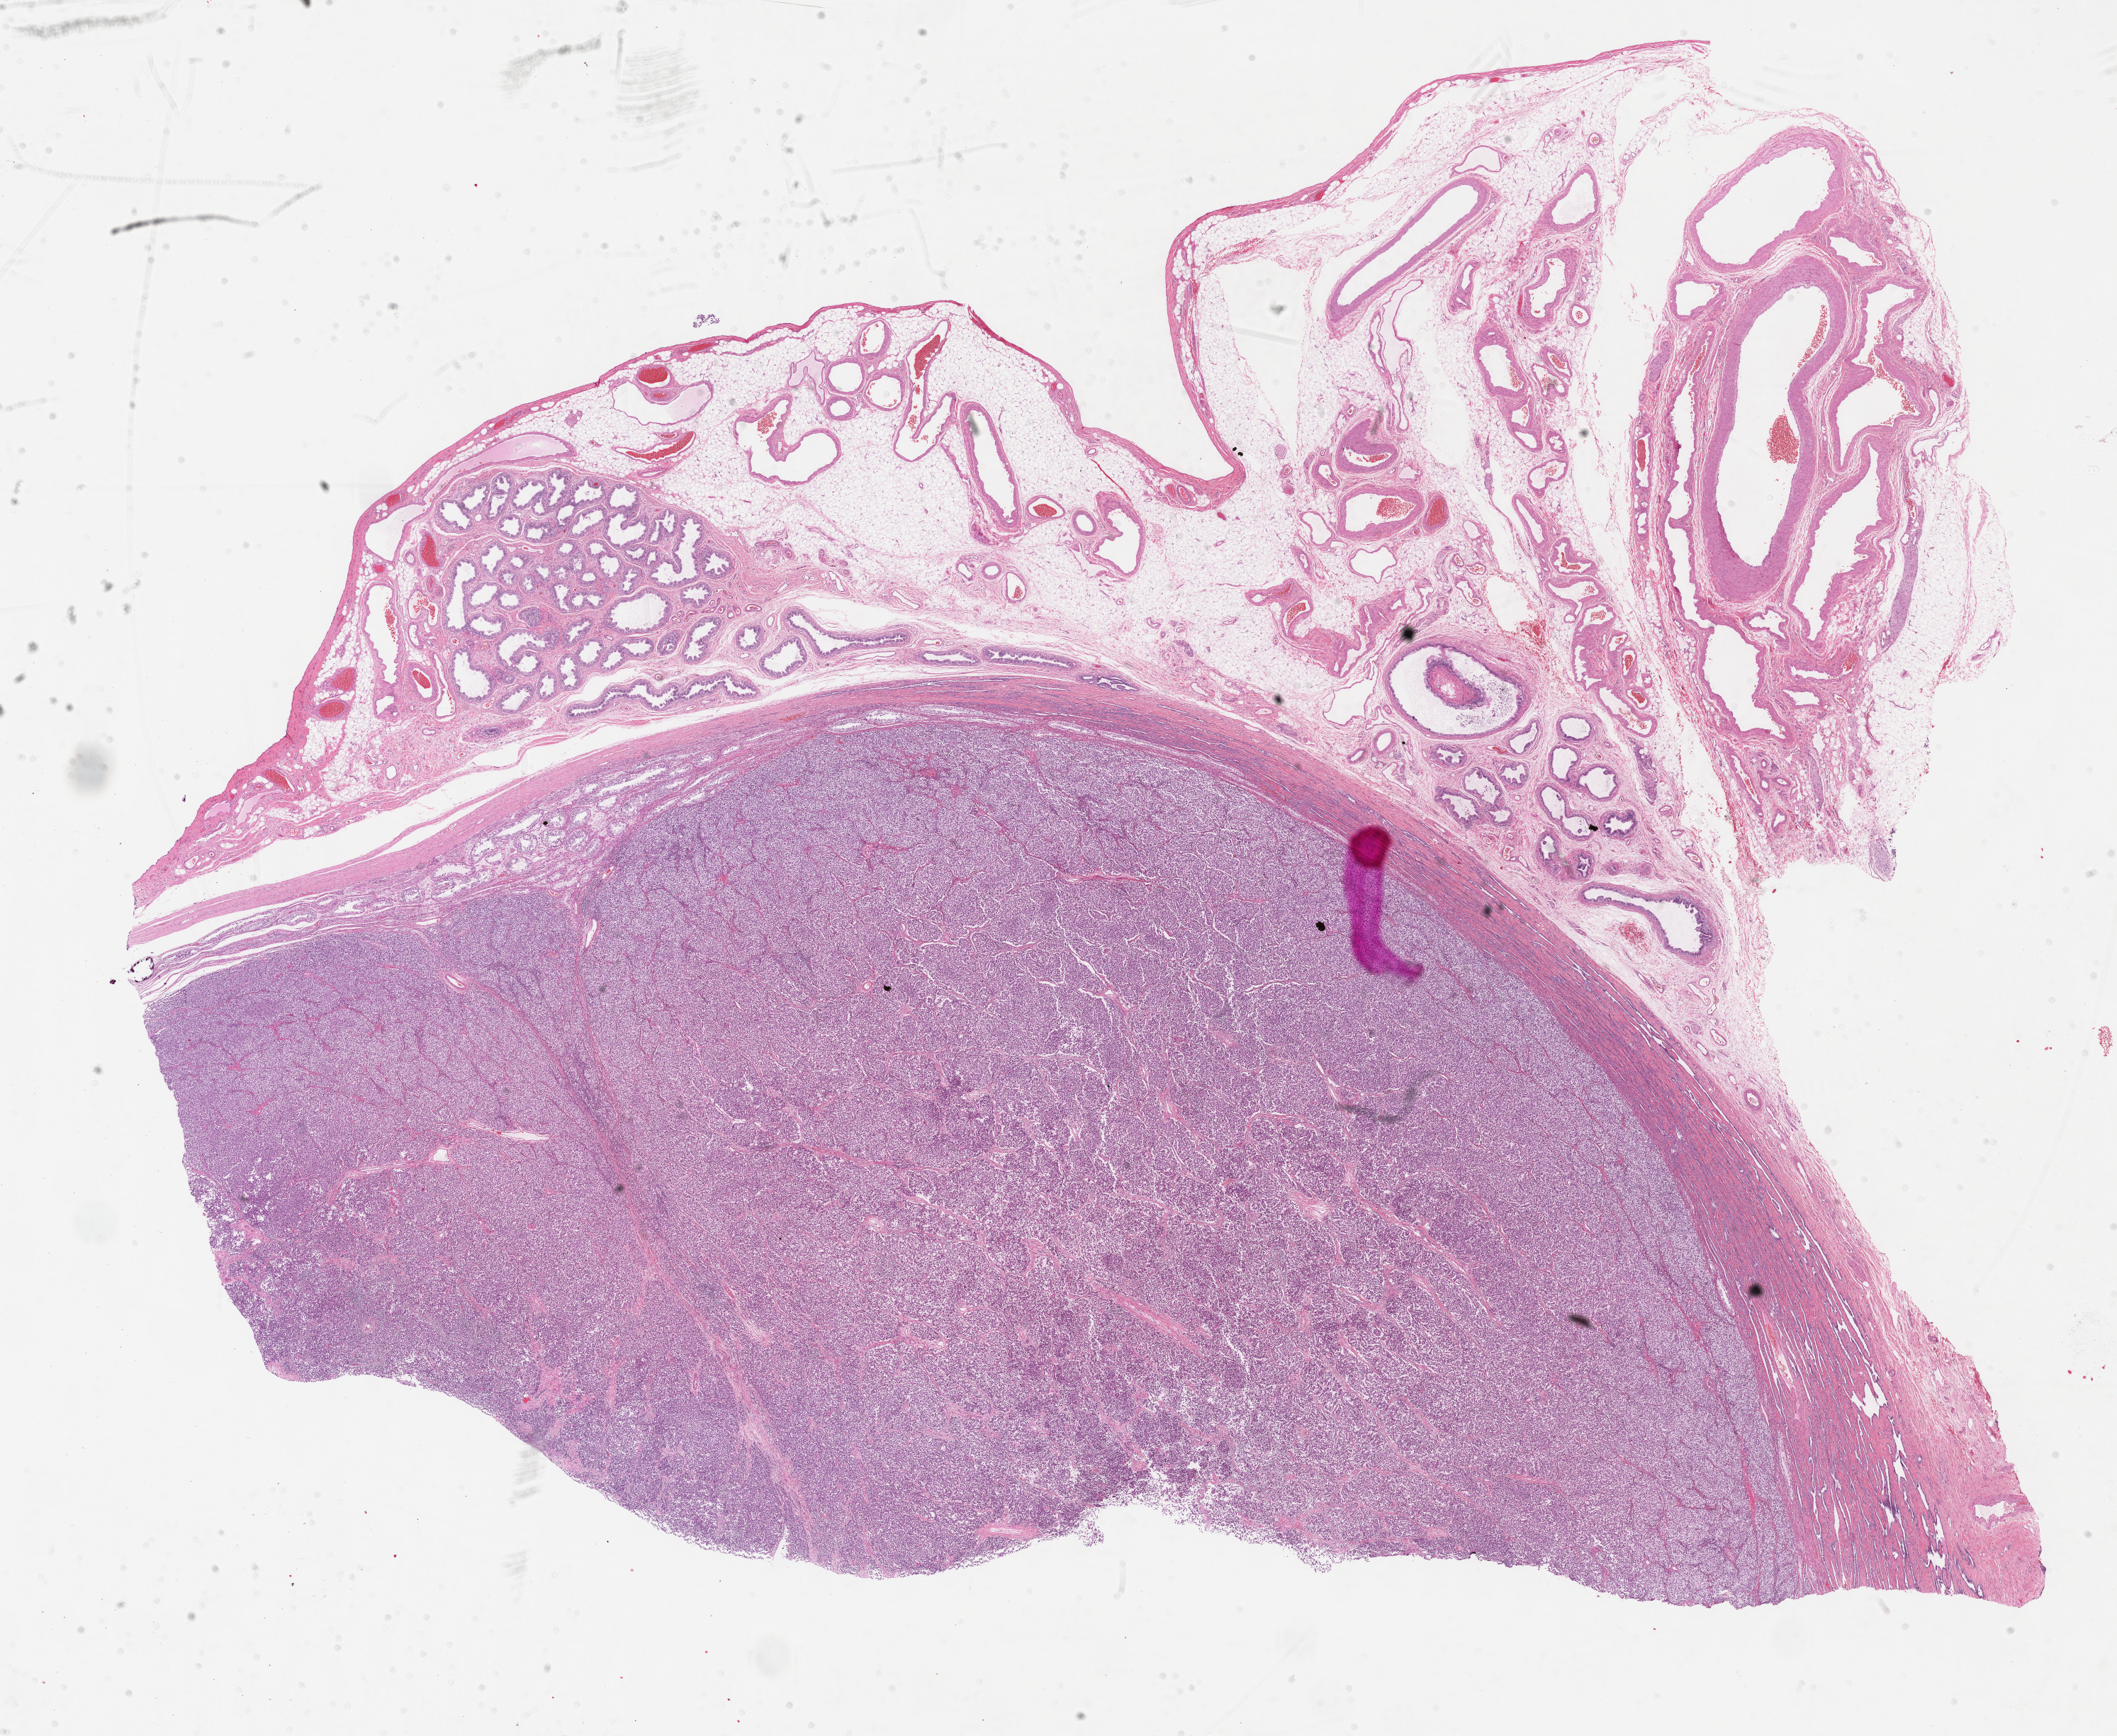
Whole-slide histology image, H&E-stained, whole scanned area (about 24.2 x 19.8 mm, acquisition: 40x scan) shown as a low-resolution overview; formalin-fixed paraffin-embedded (FFPE) diagnostic section; sample: primary tumour, testis. Male, age 38 years at initial diagnosis.
Pathologic diagnosis: Seminoma, NOS. Laterality: left.